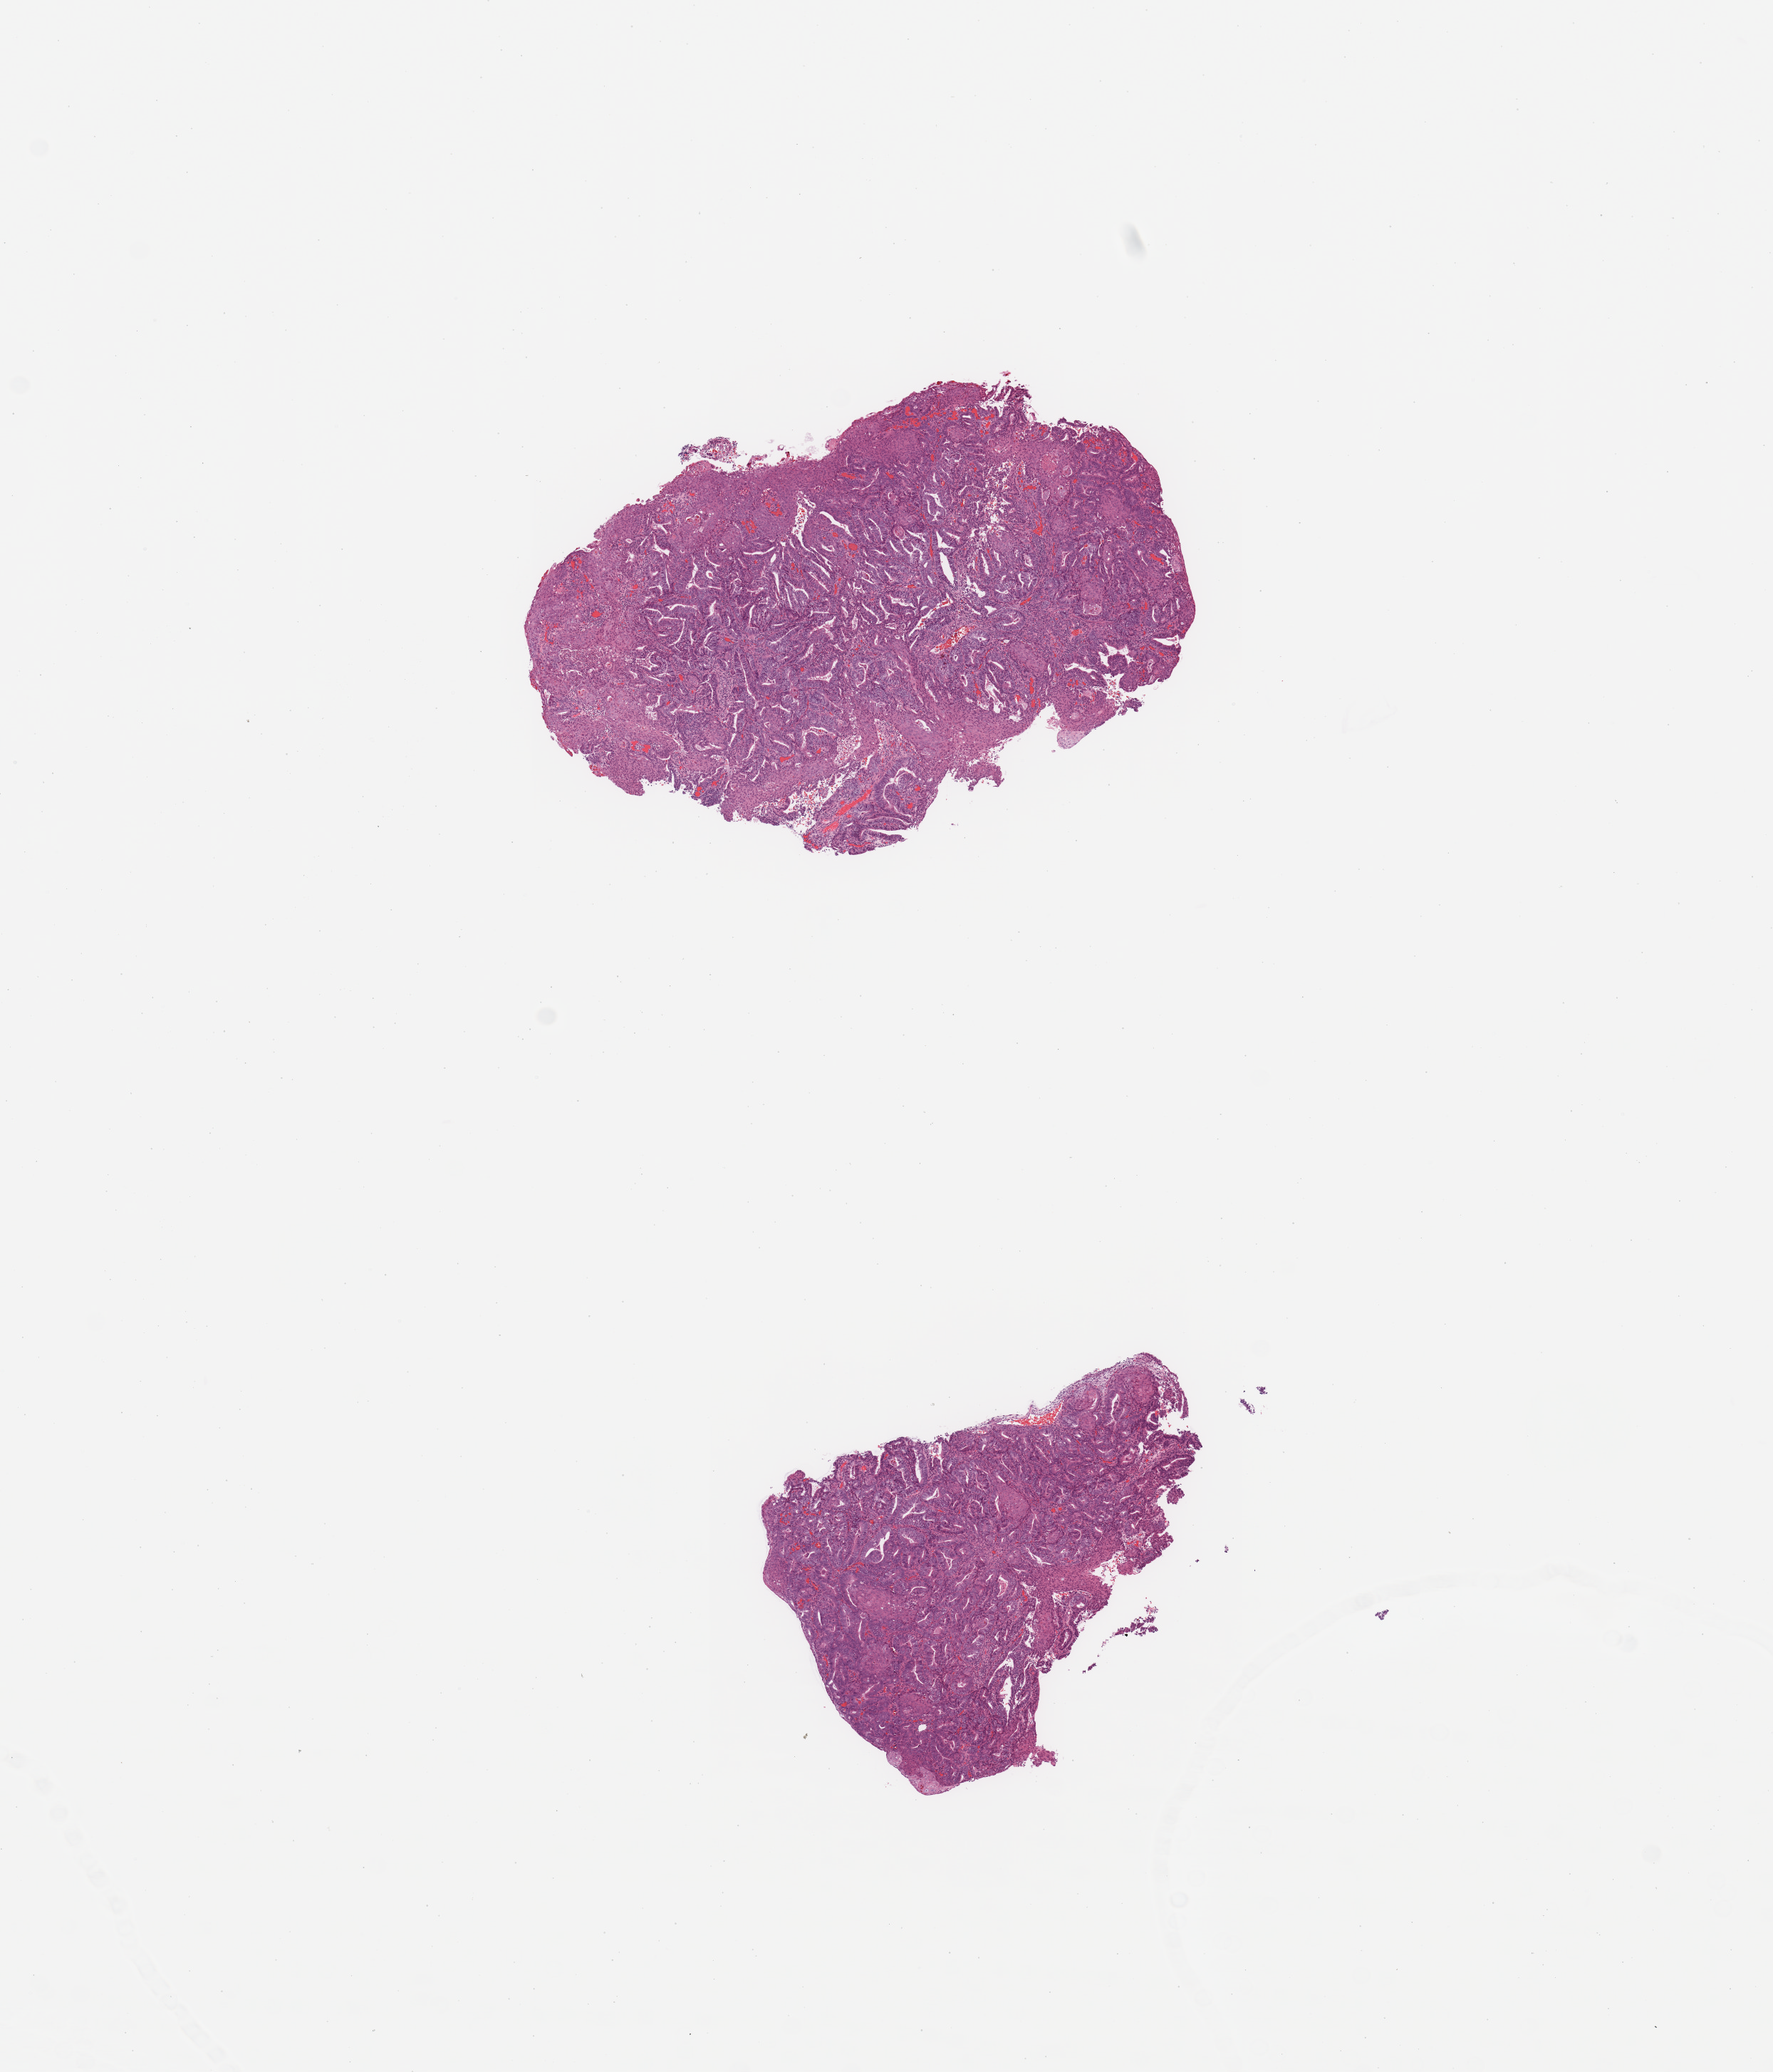
Whole-slide histology image, H&E, shown as a low-resolution overview of the whole scanned area (about 9.8 x 11.5 mm, slide scanned at 20x). Tumour tissue sample, sampled site: uterus. 56-year-old female patient. Histologic grade: G1 (well differentiated). Pathologist review of this section (percent, as recorded): tumour nuclei 95%, necrosis 2%.
• diagnosis: Endometrioid adenocarcinoma, NOS
• AJCC pathologic stage: I